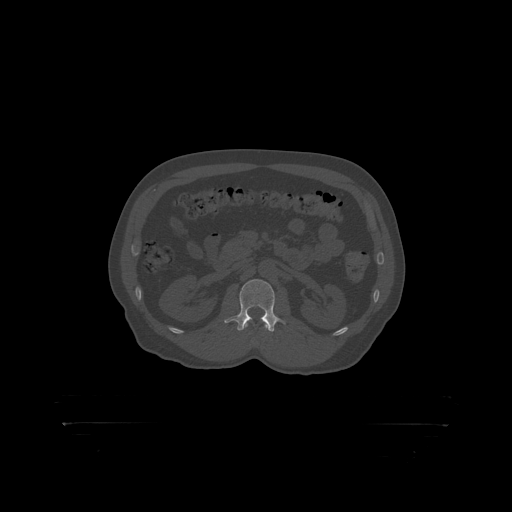
CT including the spine, one axial slice. Slice 303 of 399 in the series (ordered by position). Reconstruction kernel STANDARD. 120 kVp. Bone window (W 1800 / L 400 HU). 1.25 mm slice thickness. 512 × 512 image matrix, field of view 650 × 650 mm. Male patient, age 46 years. From the clinical record (not read from this slice): primary cancer: skin.
Annotated regions visible in this slice (semi-automatically segmented with operator editing):
- L2 vertebra: bounding box (x1, y1, x2, y2) in pixels: (238, 280, 275, 319)